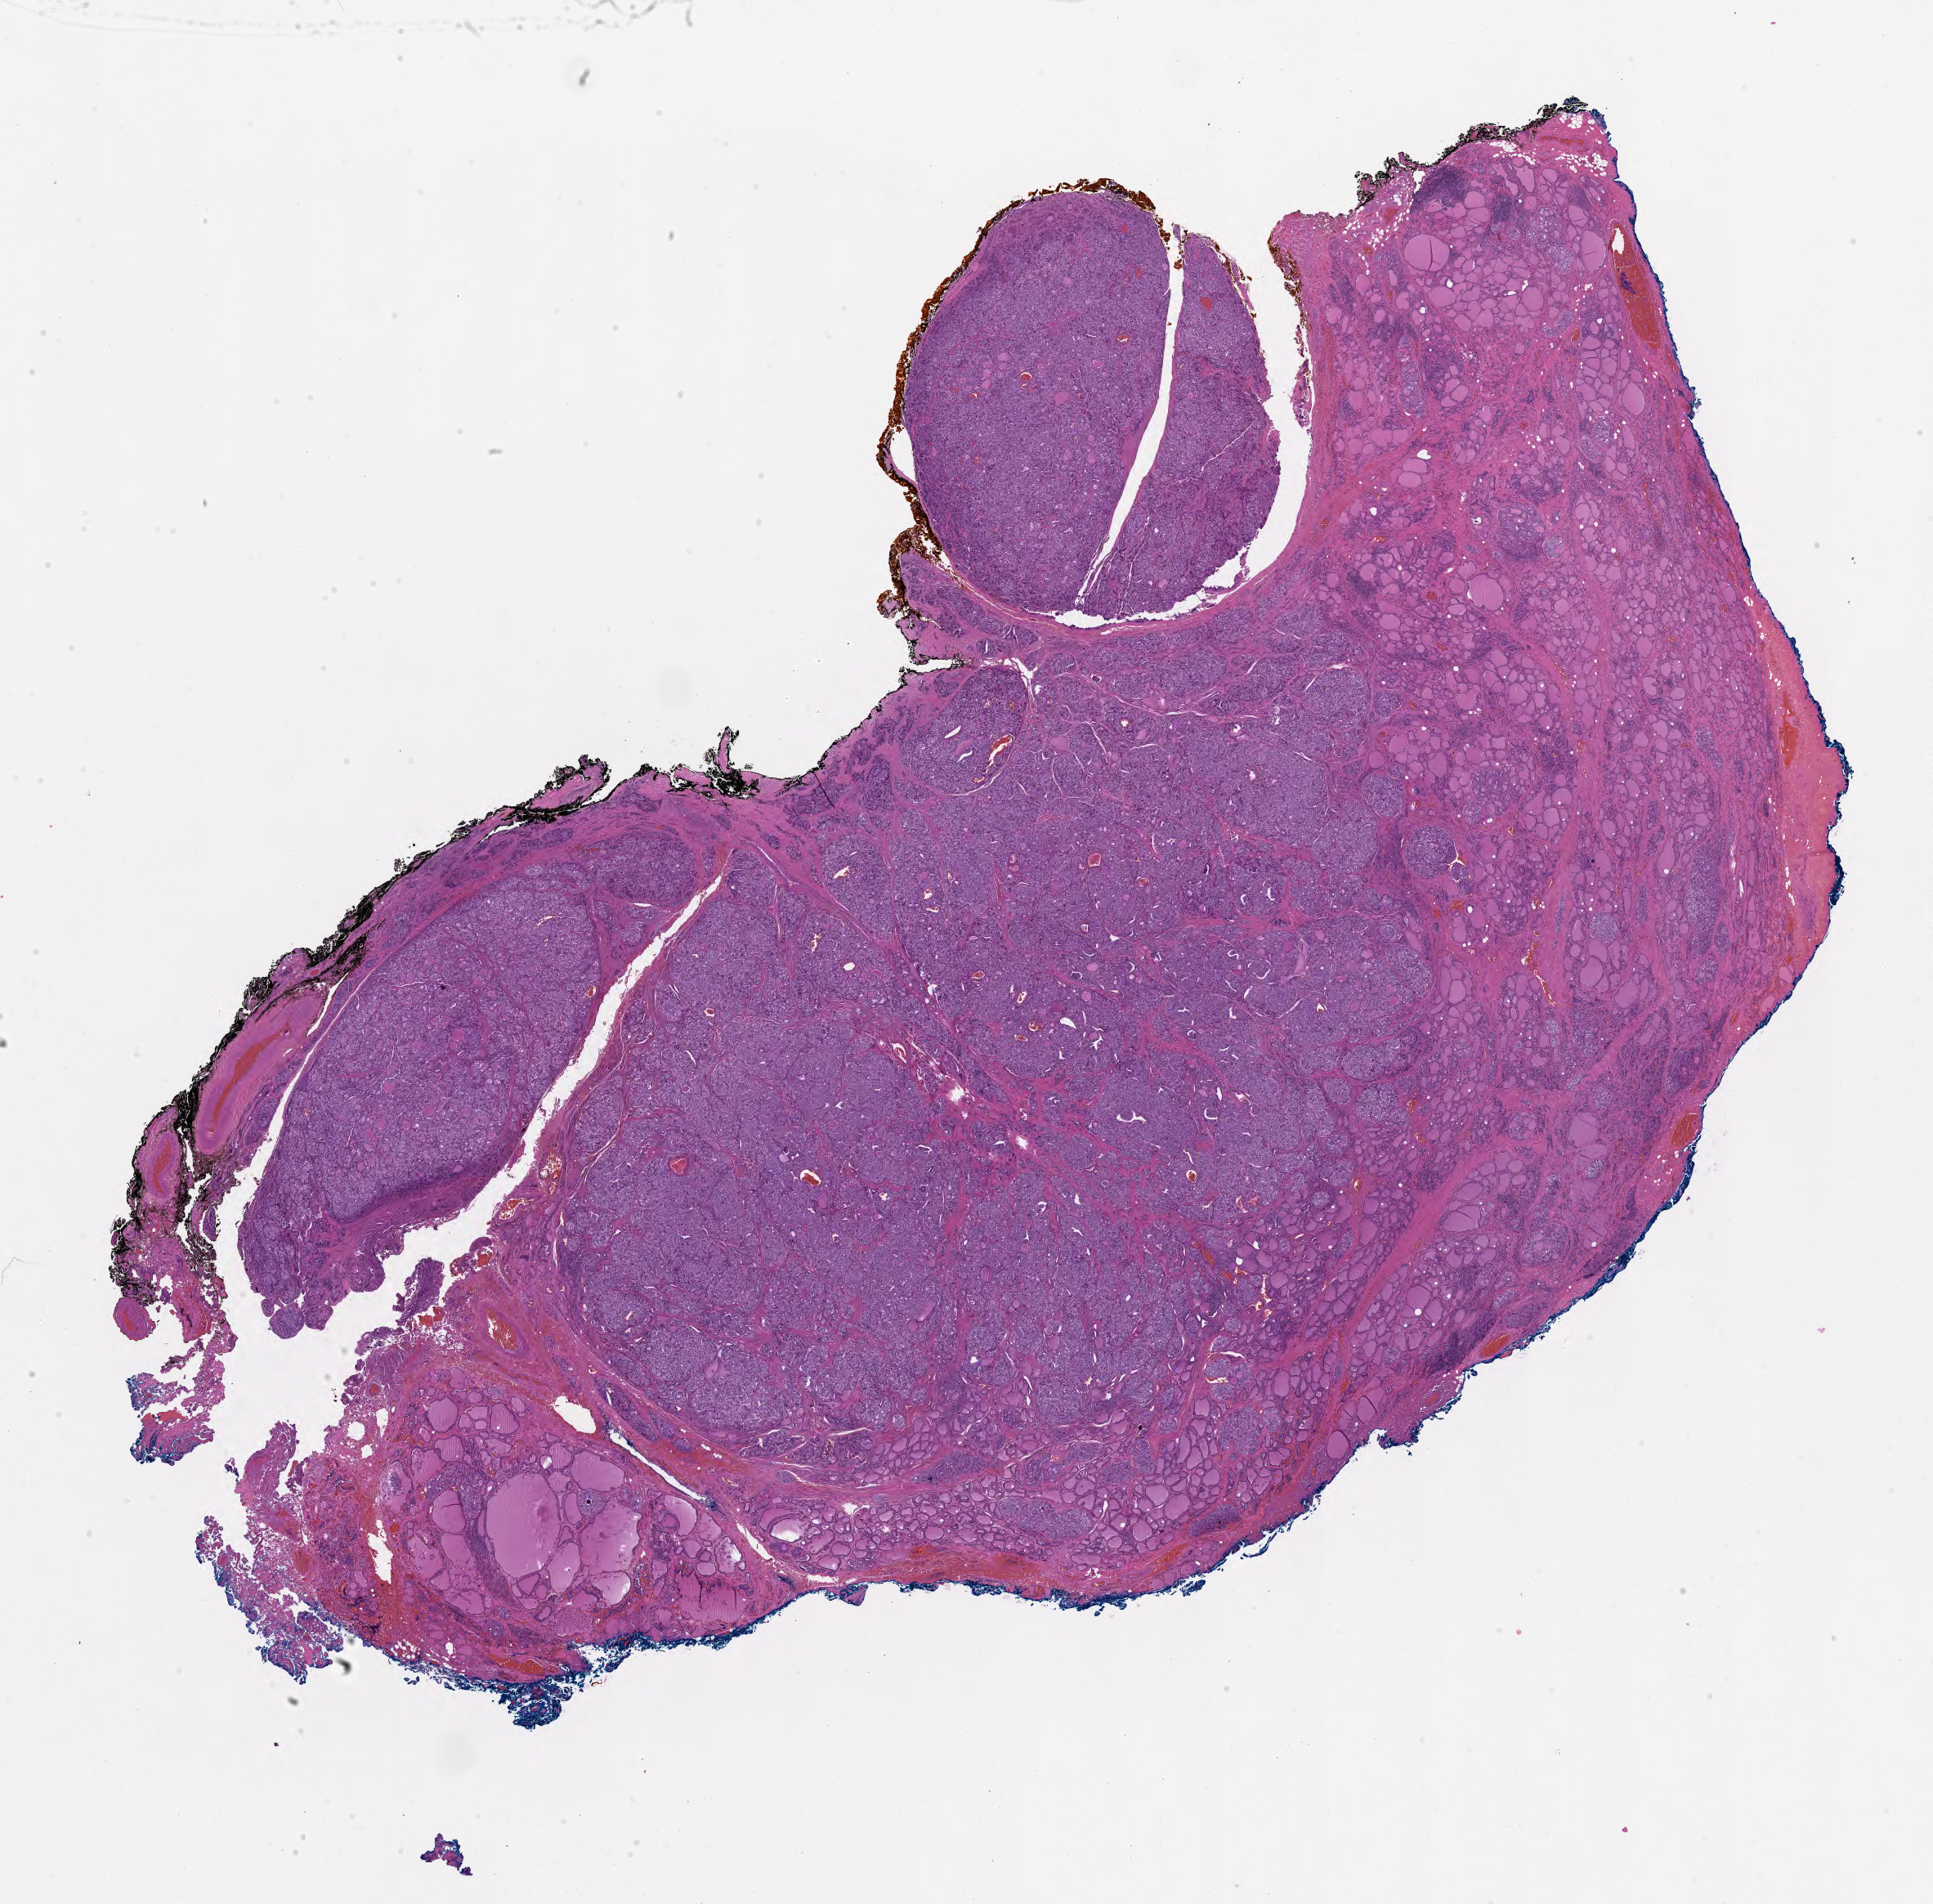
Digitized hematoxylin and eosin (H&E)-stained section of tumor tissue from the thyroid, whole scanned area (about 19.0 x 18.8 mm) shown as a low-resolution overview. Formalin-fixed paraffin-embedded section. Patient female; age 145 months.
Diagnosis (ICD-O-3 morphology term): Papillary carcinoma, NOS.